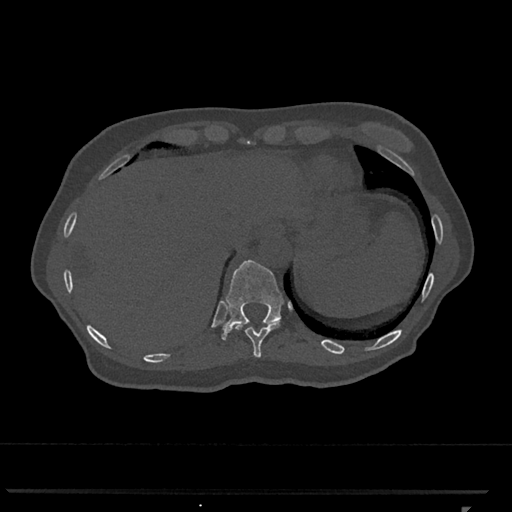
CT including the spine, one axial slice. Slice 541 of 793 in the series (ordered by position). Reconstruction kernel Br40s/3. 120 kVp. Bone window (W 1800 / L 400 HU). 0.5 mm slice thickness. 512 × 512 image matrix, field of view 380 × 380 mm. Patient: female, 62 years. From the clinical record (not read from this slice): primary cancer: renal.
Annotated regions visible in this slice (semi-automatic segmentation, software-assisted and operator-edited):
- T10 vertebra: box from (x=235, y=322) to (x=280, y=358) px
- T11 vertebra: (x=221, y=260)–(x=284, y=340)